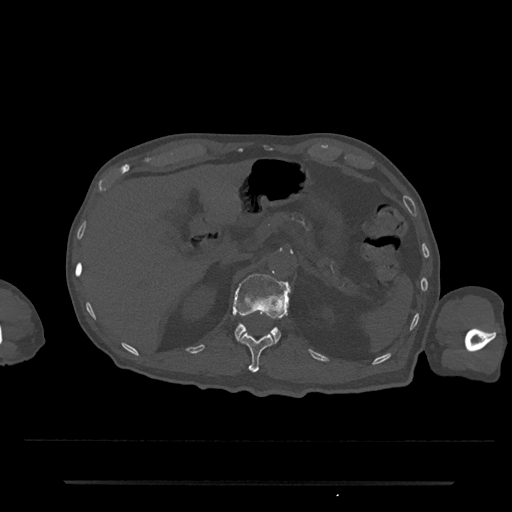
CT including the spine, one axial slice; position 167 of 797 along the scan axis; bone window (W 1800 / L 400 HU); 0.5 mm slice thickness; 512 × 512 image matrix, field of view 427 × 427 mm. Male patient, age 74 years. From the clinical record (not read from this slice): primary cancer: prostate.
Structures marked on this image (semi-automatically segmented with operator editing):
- L1 vertebra: bounding box [x1, y1, x2, y2] px = [232, 274, 291, 344]
- T12 vertebra: [240, 333, 274, 373]